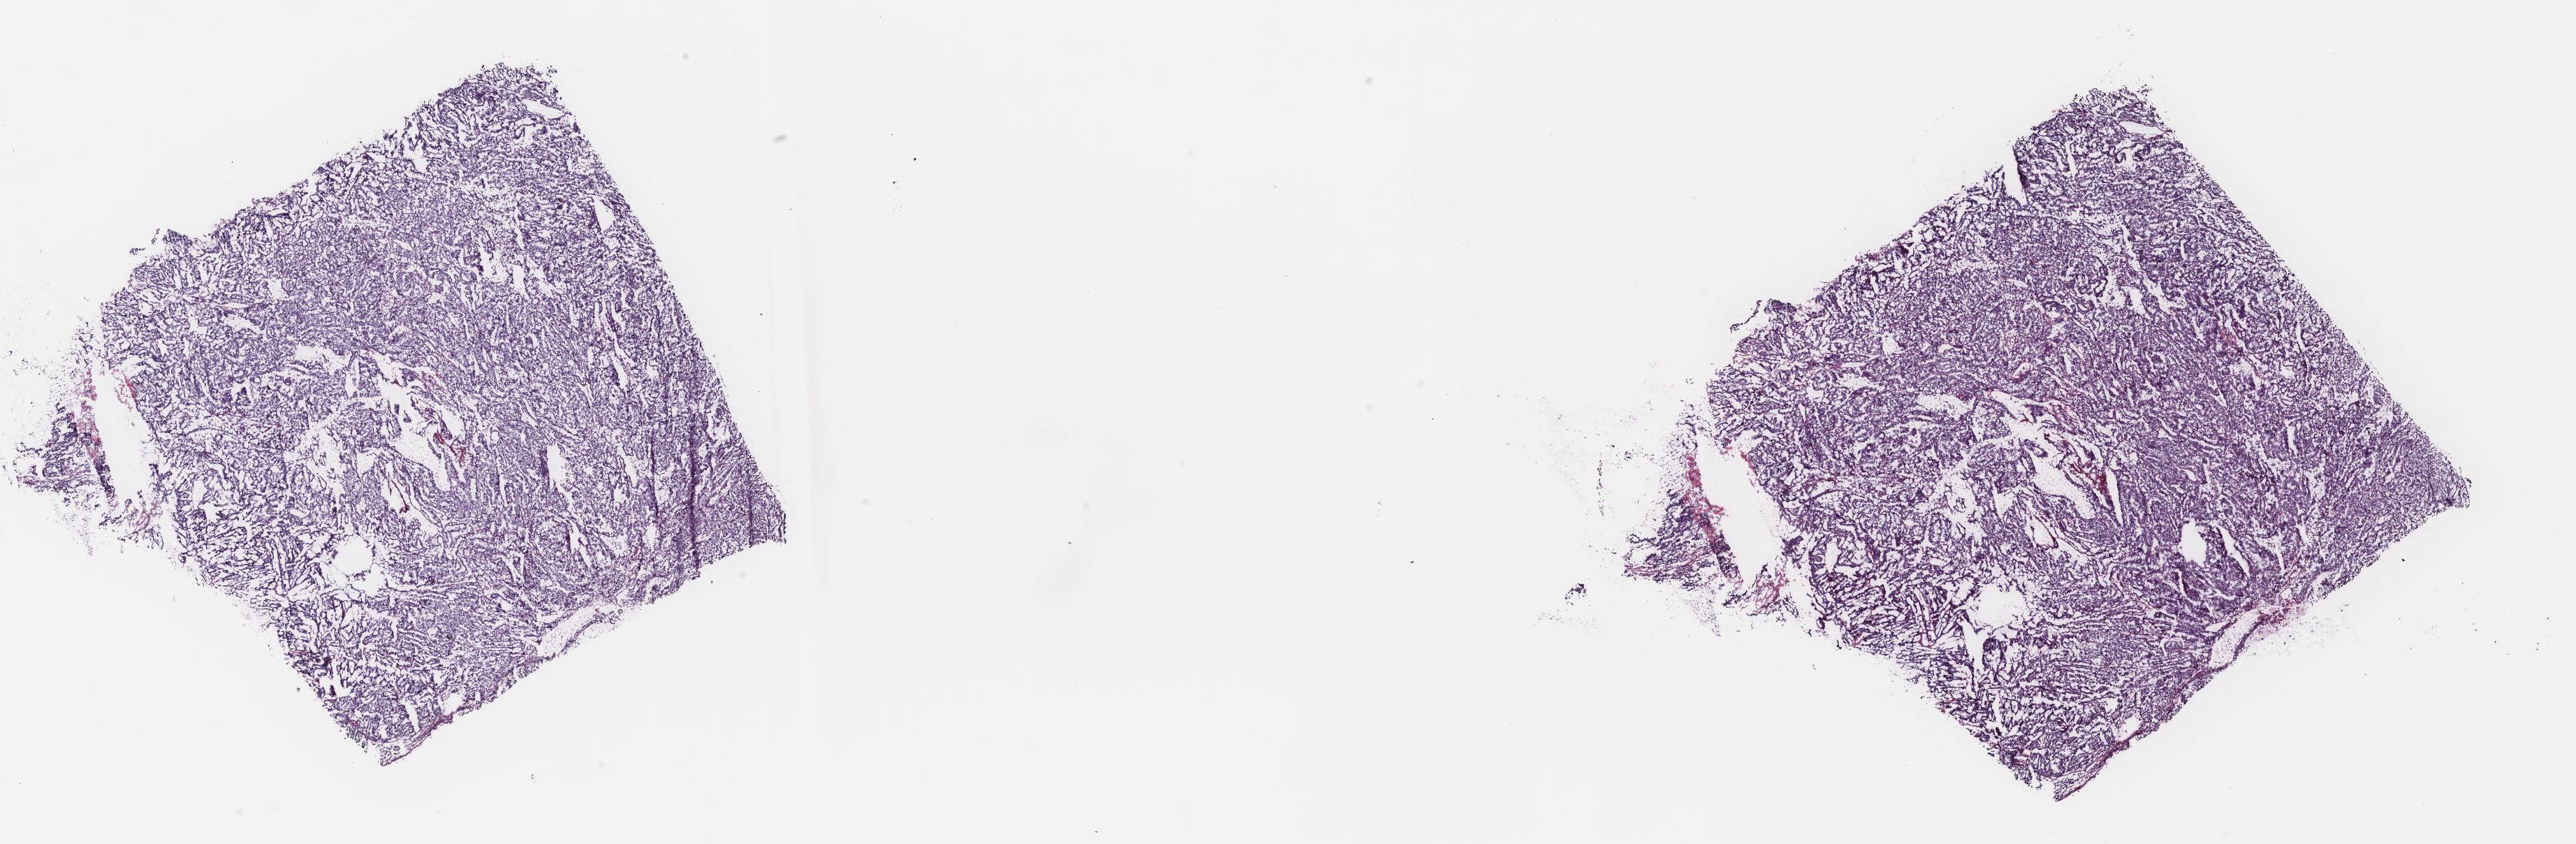
Digitized H&E tissue section (whole slide) — low-resolution overview of the scanned area, about 29.3 x 9.6 mm. Frozen section from the top of the tissue portion. Primary tumour sample from the uterus. Female, age 67 years at initial diagnosis. Histologic grade: G3 (poorly differentiated). Composition of this section per pathologist review: tumour cells 96%, tumour nuclei 98%, normal cells 0%, stromal cells 2%, necrosis 2%. Inflammatory infiltration, as recorded: lymphocyte infiltration 0%, monocyte infiltration 0%, neutrophil infiltration 0%.
Diagnosis: Serous cystadenocarcinoma, NOS (endometrium). FIGO stage: IB. Lymph nodes positive (case pathology): 0 of 9 examined.